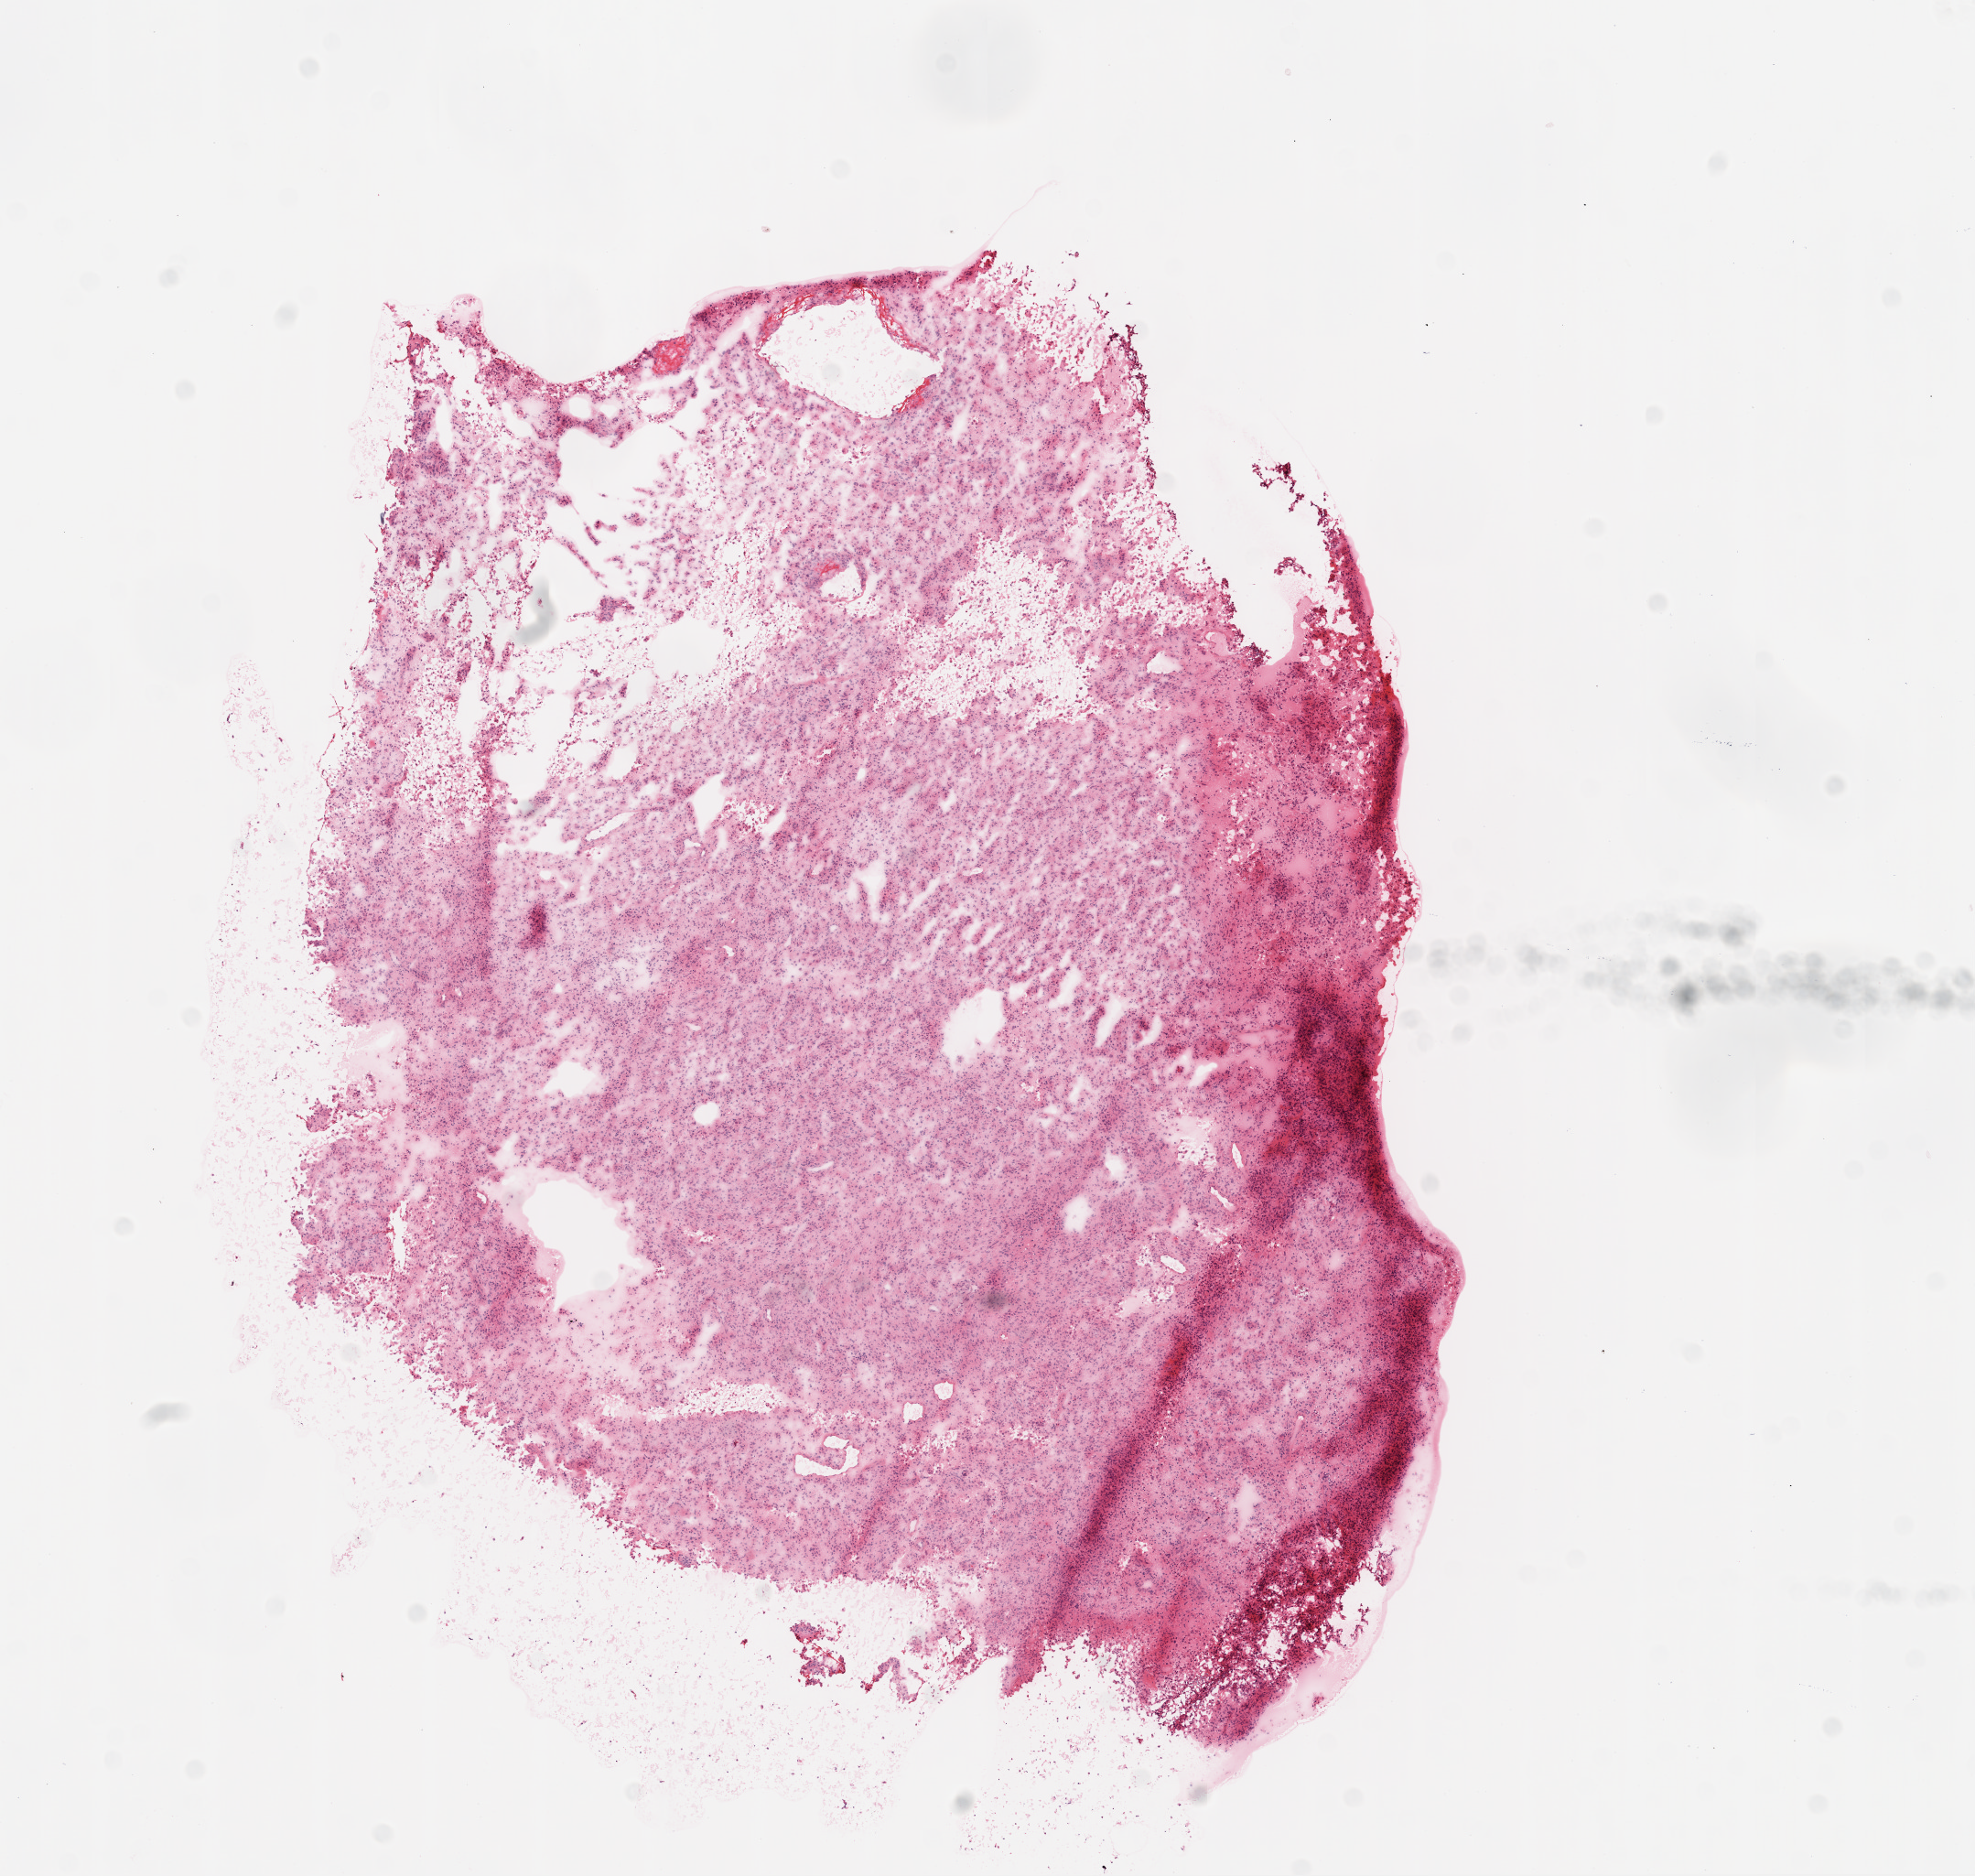
Whole-slide histology image, H&E — shown as a low-resolution overview of the whole scanned area (about 8.7 x 8.3 mm, from a 20x scan). Frozen section from the top of the tissue portion. Primary tumour sample from the brain. Male, age 69 years at initial diagnosis. Composition of this section per pathologist review: tumour cells 85%, tumour nuclei 90%, normal cells 0%, stromal cells 0%, necrosis 15%.
- diagnosis: Glioblastoma